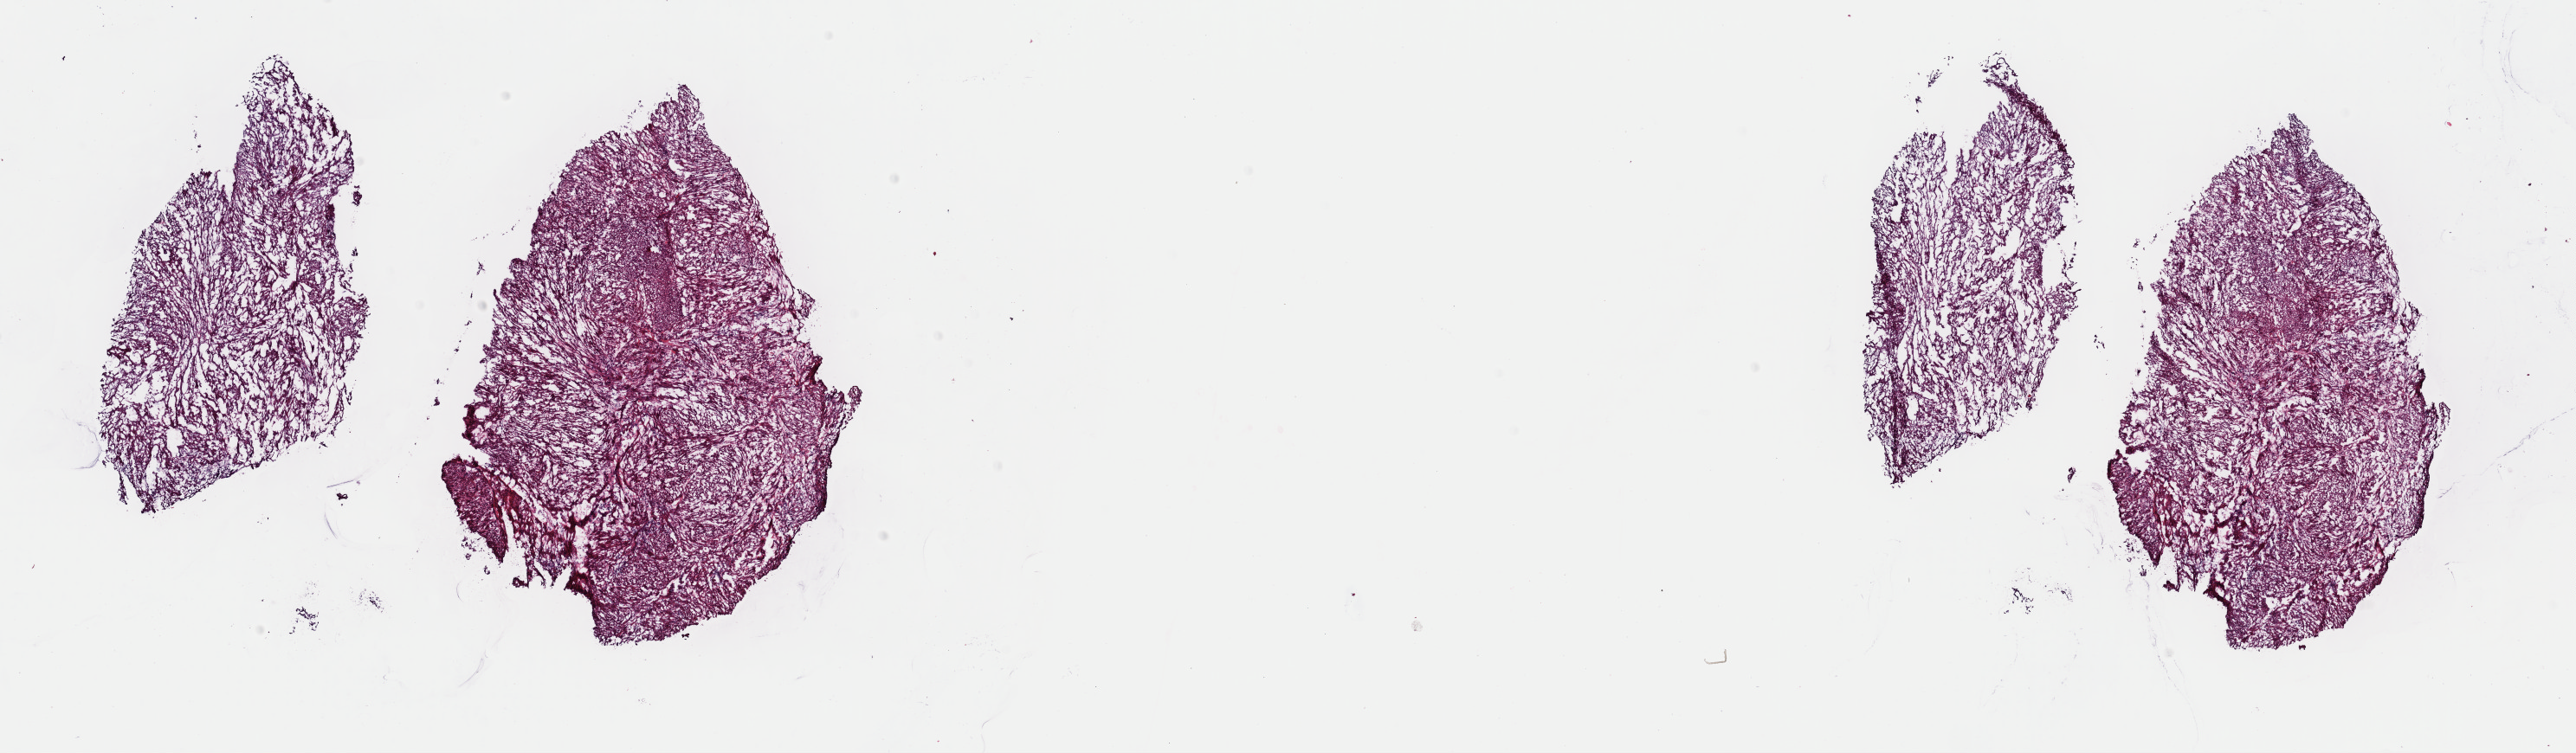
Digitized H&E tissue section (whole slide) — a low-resolution overview of the entire scanned area, about 23.5 x 6.9 mm. Frozen section from the top of the tissue portion. Connective, subcutaneous and other soft tissues, primary tumour sample. Female patient; age at initial diagnosis 82 years. Composition of this section per pathologist review: tumour cells 65%, tumour nuclei 100%, normal cells 0%, stromal cells 35%, necrosis 0%. Inflammatory infiltration, as recorded: lymphocyte infiltration 0%, monocyte infiltration 1%, neutrophil infiltration 0%.
Pathologic diagnosis: Leiomyosarcoma, NOS (connective, subcutaneous and other soft tissues of lower limb and hip).